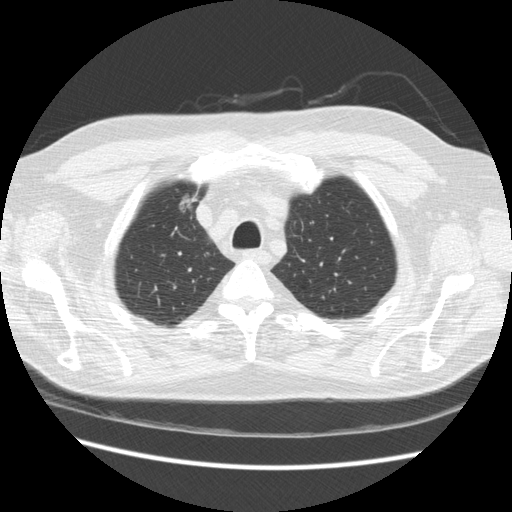
Low-dose screening chest CT, axial slice. Third screening round (two years after baseline). Lung window (W 1500 / L -600 HU). 2.5 mm slice thickness. Standard (soft-tissue) reconstruction kernel (STANDARD). 512 × 512 image matrix, field of view 360 × 360 mm. Male, age 66 years at enrolment. Former smoker at enrolment.
- Expert reader's lesion annotation, box from (x=167, y=184) to (x=209, y=221) px.
- No non-calcified nodule or mass ≥4 mm was recorded by the screening reader at this exam.
- Official screen result: positive, other.
- Participant outcome: lung cancer diagnosed 229 days after this screen — bronchiolo-alveolar adenocarcinoma, NOS, right upper lobe, moderately differentiated (G2), stage IA (AJCC 6th edition), 12 mm at pathology.